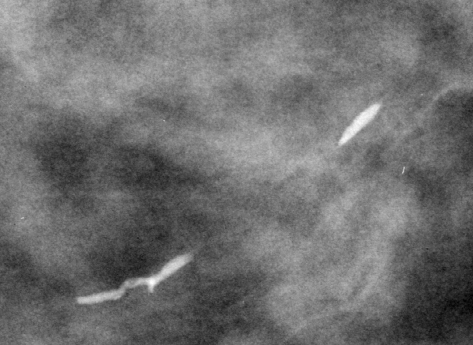
Crop from a digitized film mammogram around one marked abnormality, left breast, CC view.
Calcifications, morphology large rodlike / round and regular, distribution regional; BI-RADS assessment category 2; benign; no additional work-up was recommended (benign without callback).